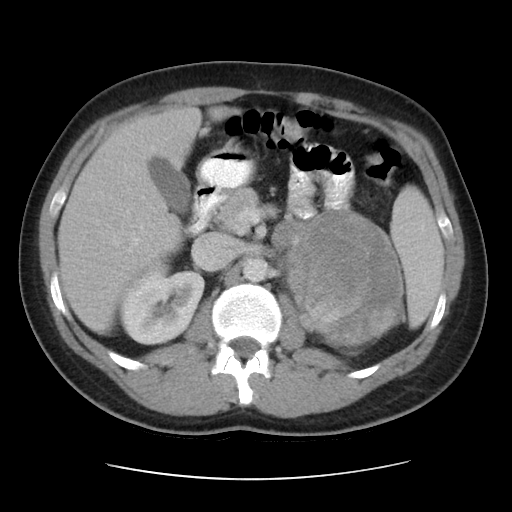
Contrast-enhanced abdominal CT, one axial slice. Position 25 of 48 along the scan axis. Reconstruction kernel STANDARD. 120 kVp. Intravenous contrast given. Soft-tissue window (W 400 / L 40 HU). 5 mm slice thickness. 512 × 512 image matrix, field of view 360 × 360 mm. Male patient, age 32 years. Case-level facts recorded for this patient, not image findings: diagnosis: adrenocortical carcinoma; tumour side: left adrenal; tumour size at pathology: 14 cm; Ki-67 index: 67 %; stage (as recorded): 3.
Outlined on this slice (semi-automatically segmented with operator editing):
- mass: bounding box [x1, y1, x2, y2] px = [290, 213, 401, 351]